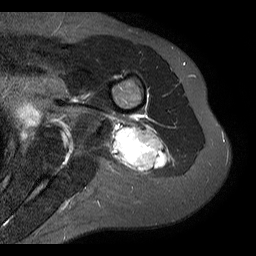
MRI of an extremity soft-tissue mass, one axial slice. Position 8 of 20 along the scan axis. STIR. 4 mm slice thickness. 256 × 256 image matrix, field of view 150 × 150 mm. Female patient. From the clinical record (not read from this slice): histological type: malignant fibrous histiocytoma; grade: low; site of the primary tumour: left arm.
Structures marked on this image (manually delineated by an expert):
- gross tumour volume (mass): bounding box [x1, y1, x2, y2] px = [110, 118, 170, 173]